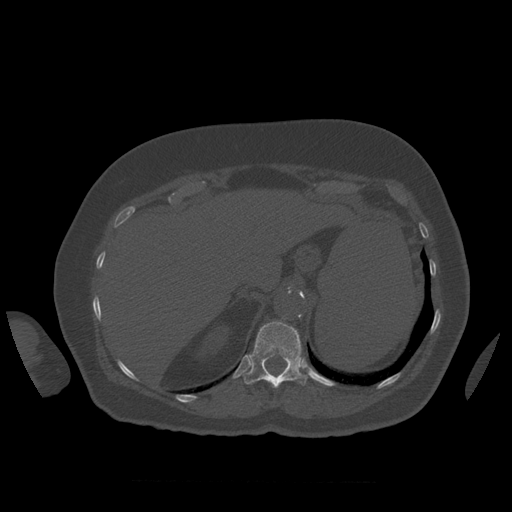
CT including the spine, one axial slice. Slice 303 of 399 in the series (ordered by position). Reconstruction kernel STANDARD. 120 kVp. Bone window (W 1800 / L 400 HU). 1.25 mm slice thickness. 512 × 512 image matrix, field of view 404 × 404 mm. Patient age 81 years. Case-level facts recorded for this patient, not image findings: primary cancer: renal.
Structures marked on this image (semi-automatically segmented with operator editing):
- T12 vertebra: bounding box <244,322,307,389> (left, top, right, bottom; pixels)